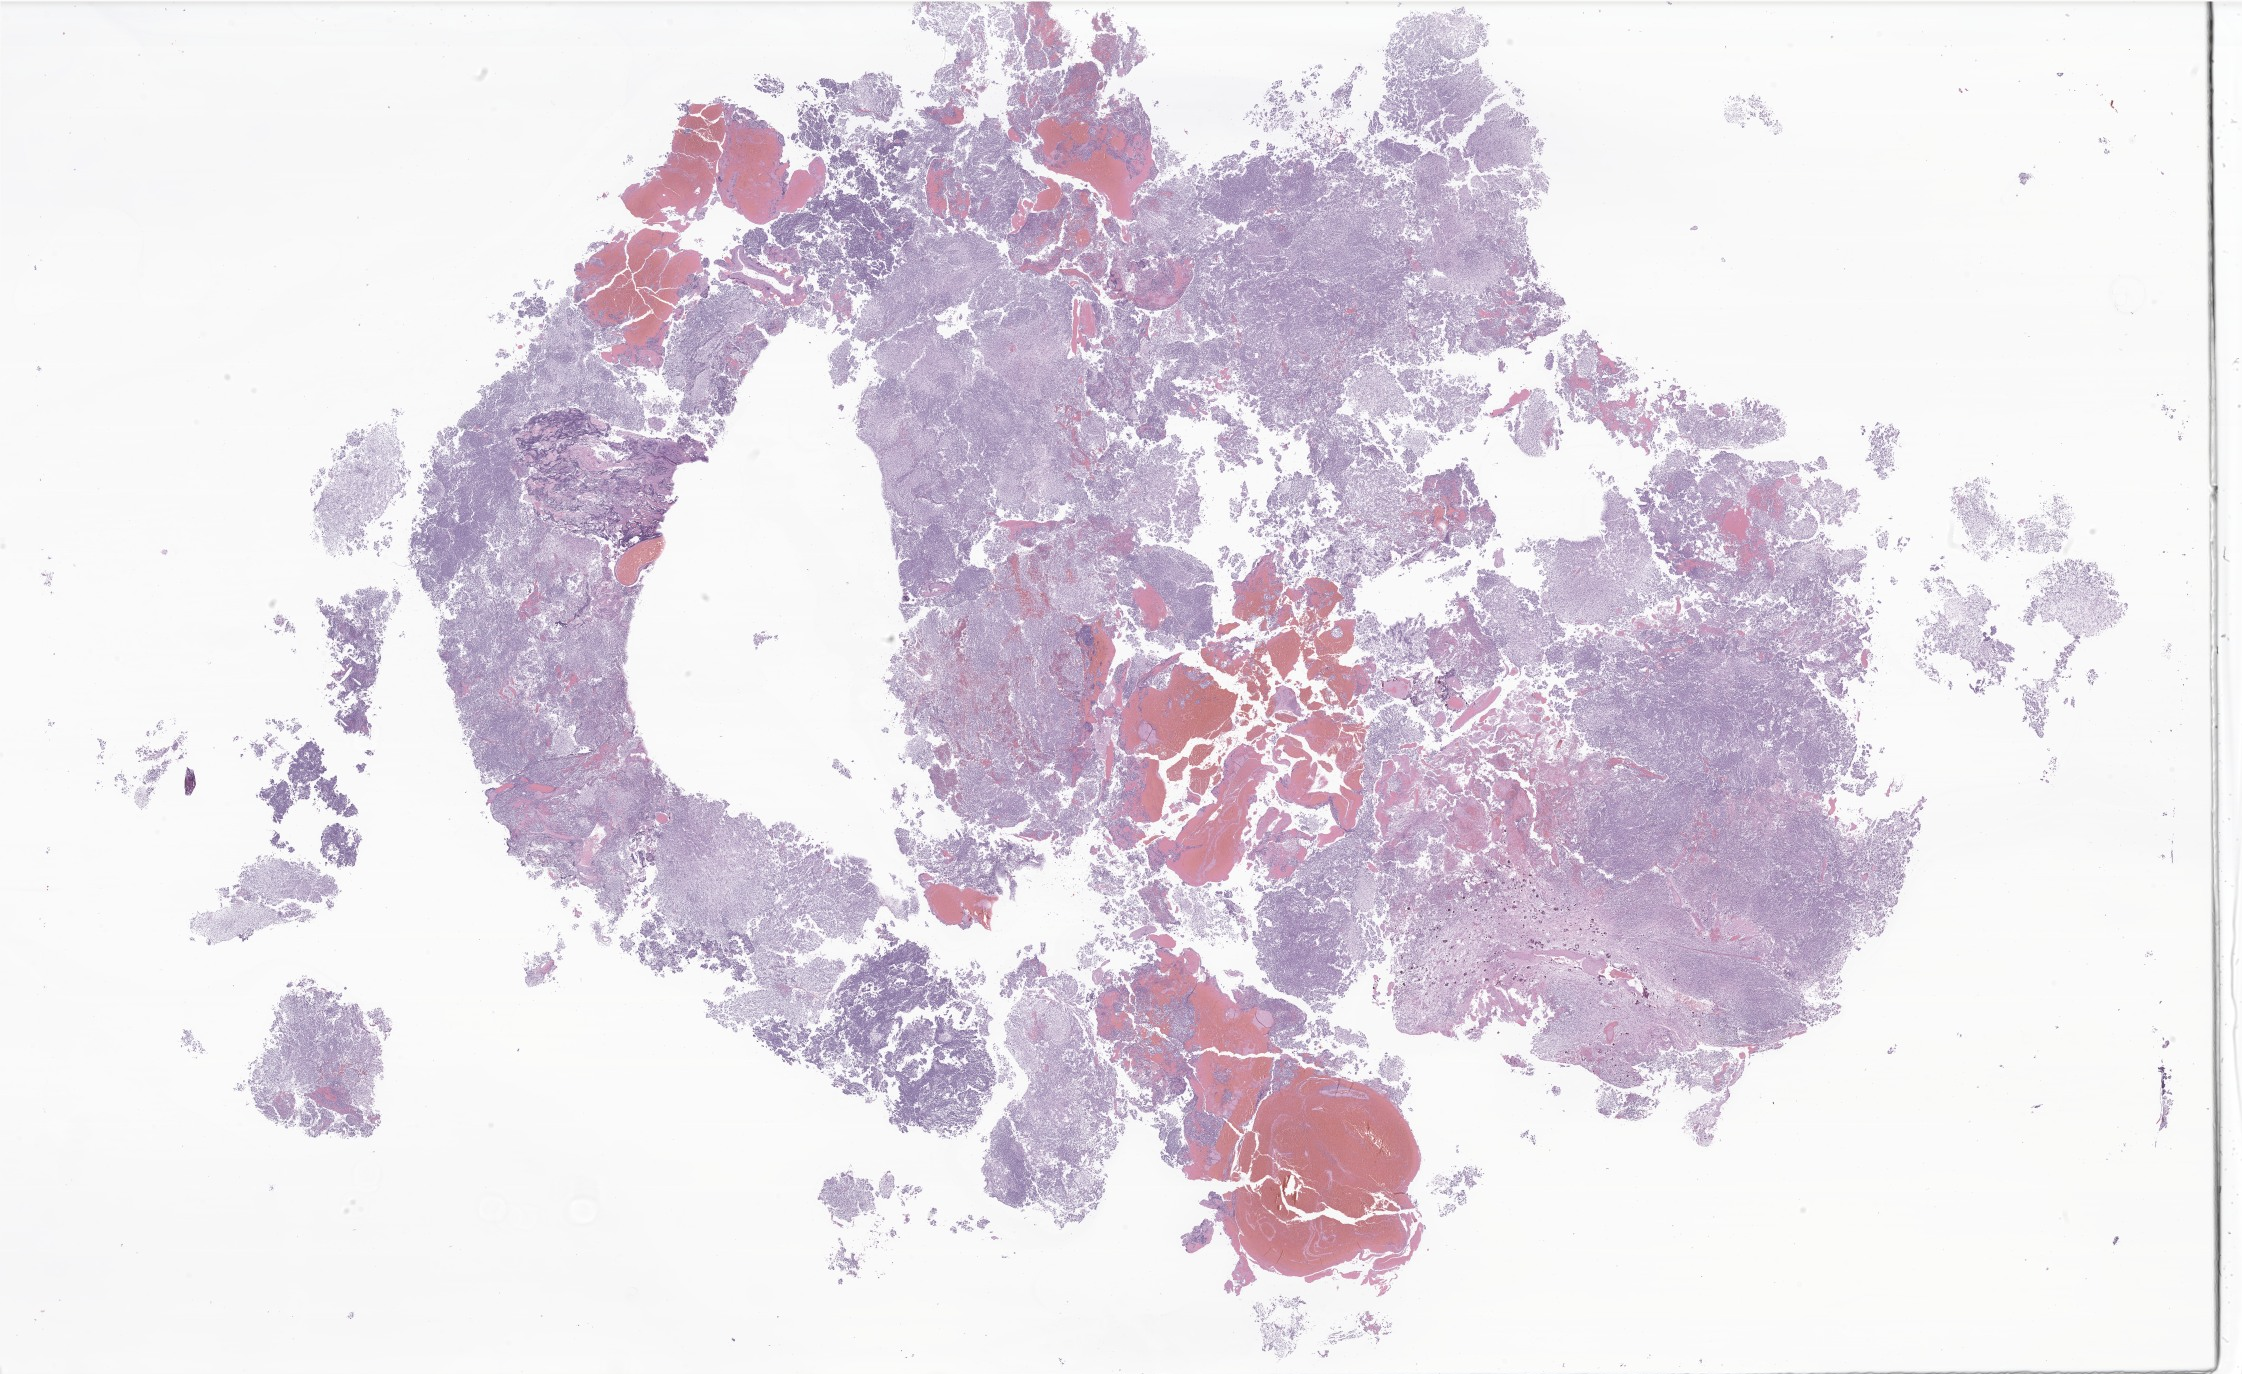
Haematoxylin and eosin whole-slide image of tumor tissue from the brain — whole scanned area (about 37.8 x 23.2 mm) shown as a low-resolution overview; formalin-fixed, paraffin-embedded (FFPE) tissue. Patient: male, age 59 months (4 years 11 months).
Diagnosis: Neoplasm, malignant.